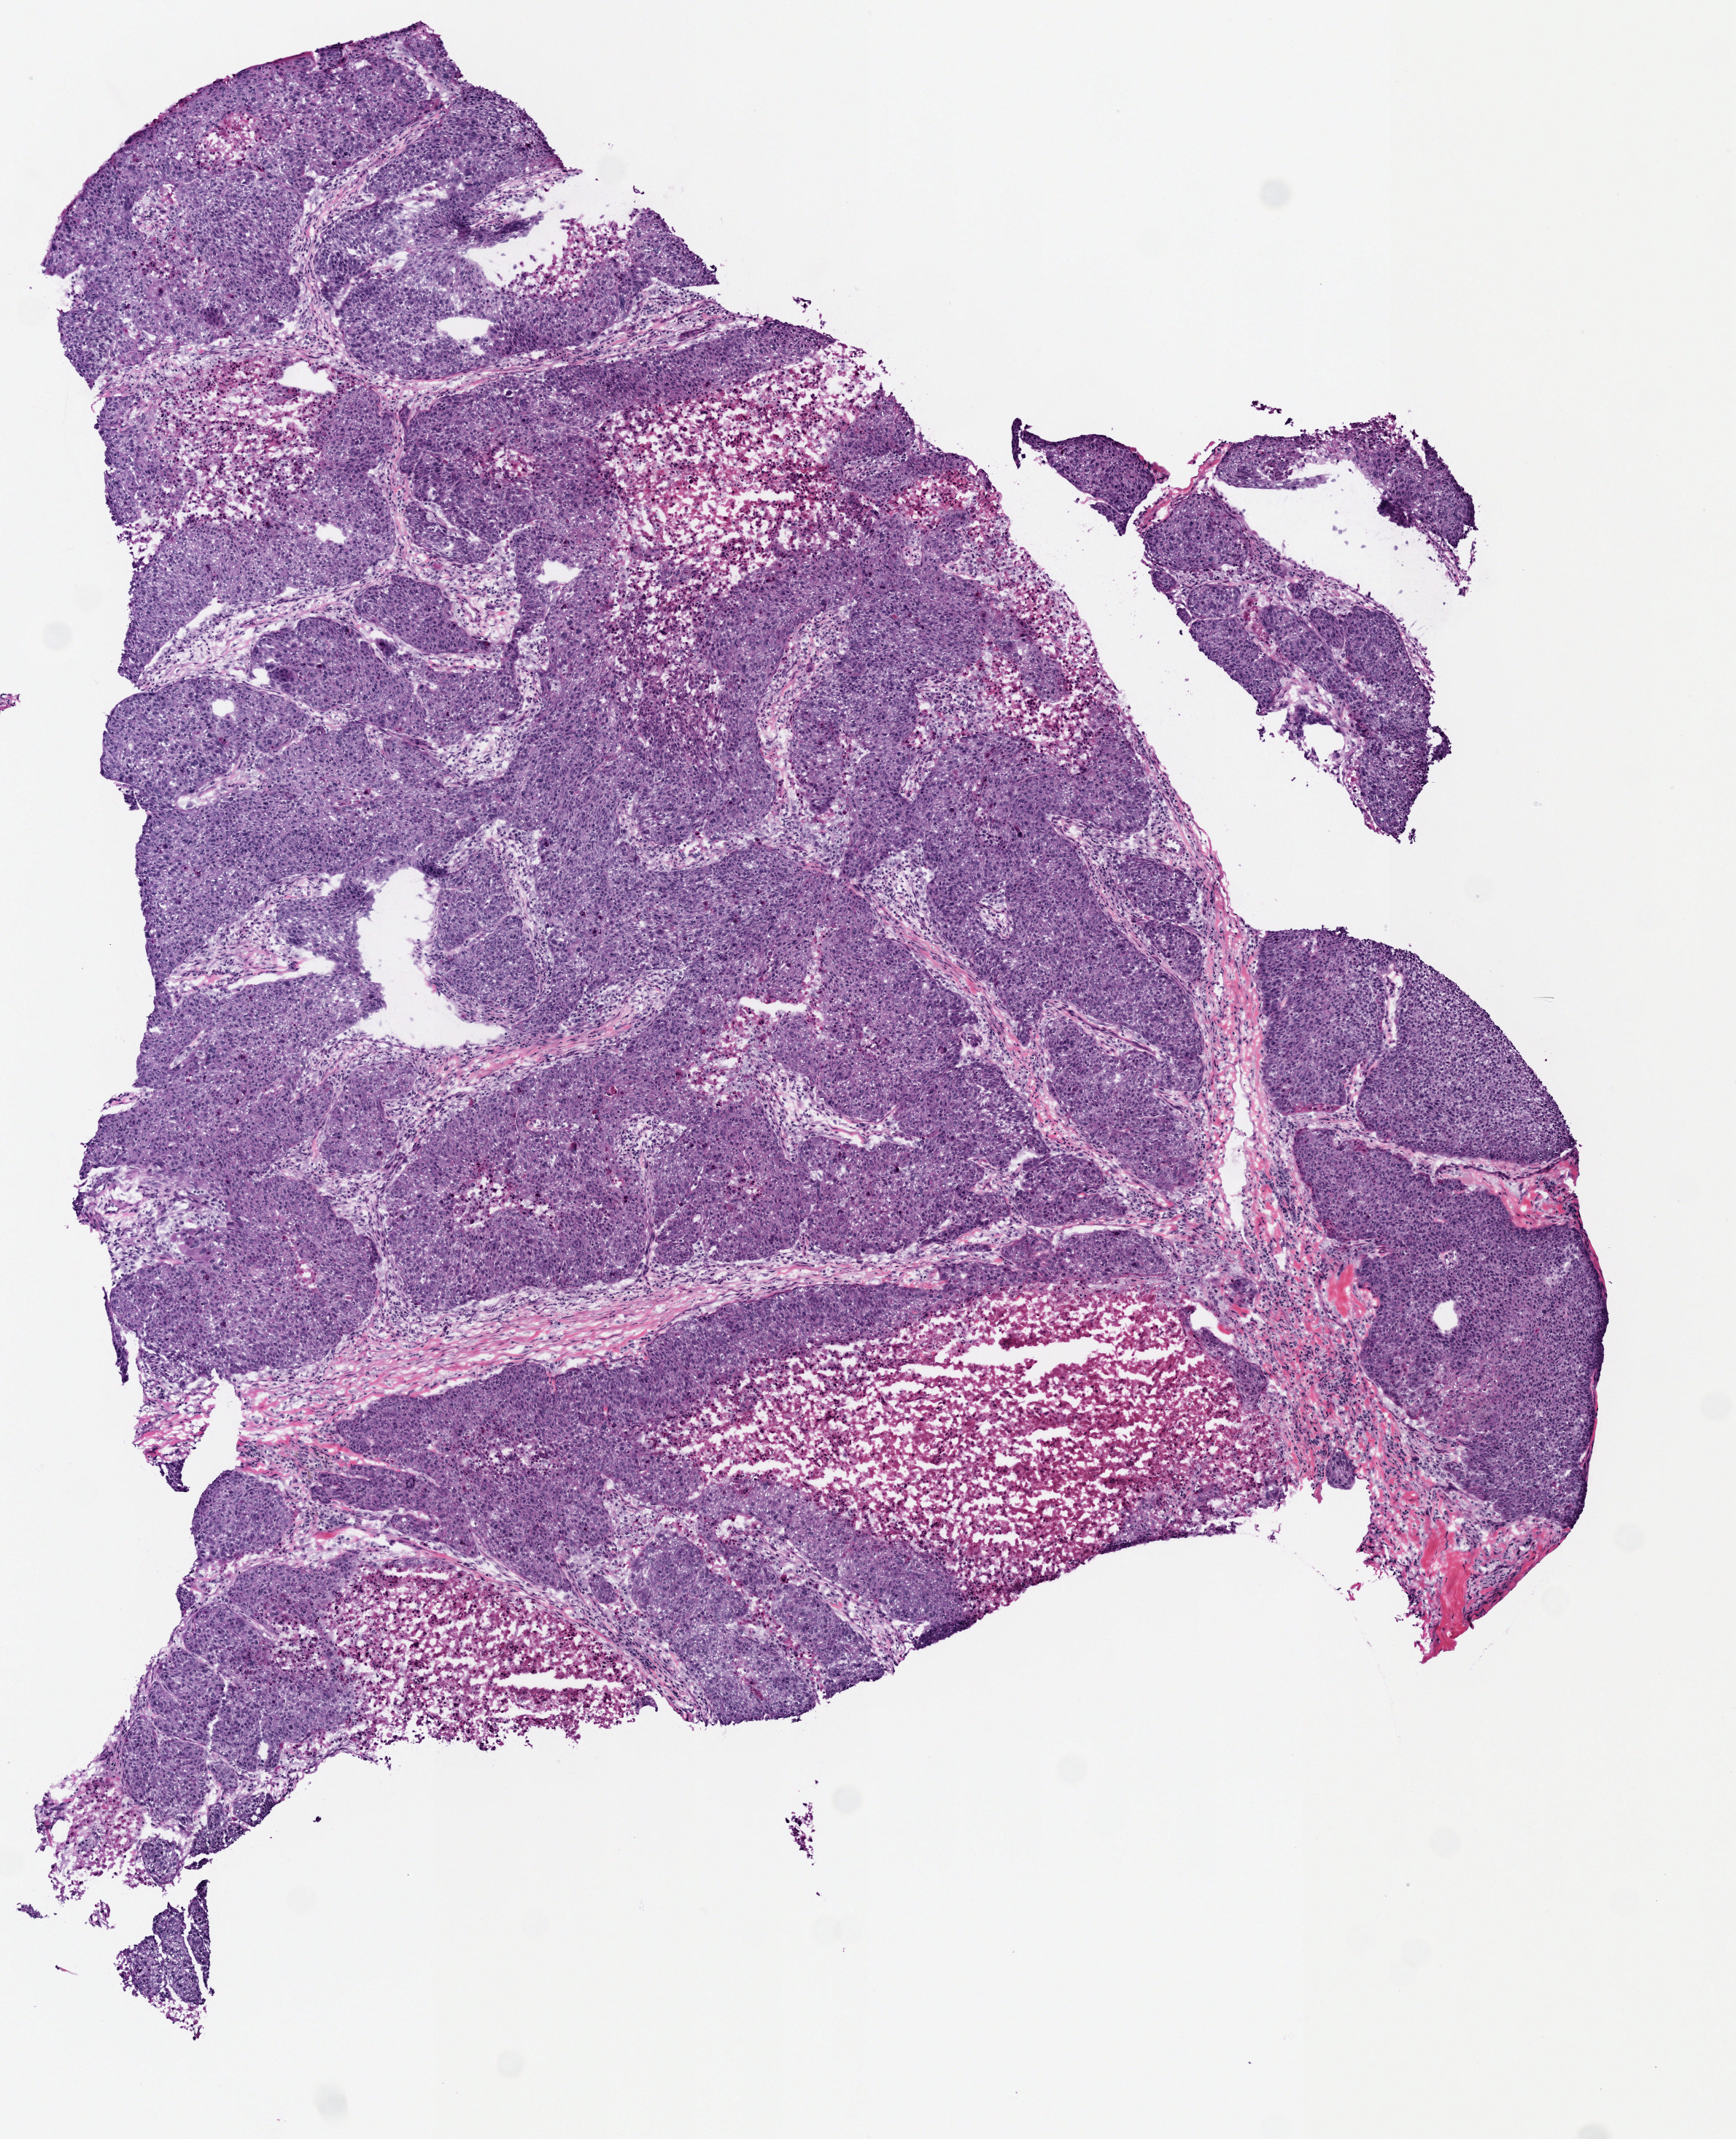
Hematoxylin and eosin (H&E) stained whole-slide image — whole scanned area (about 4.7 x 5.8 mm) shown as a low-resolution overview. Frozen section from the top of the tissue portion. Sample: primary tumour, head and neck. Male, age 49 years at initial diagnosis. Histologic grade: G2 (moderately differentiated). Composition of this section per pathologist review: tumour cells 70%, tumour nuclei 80%, normal cells 0%, stromal cells 20%, necrosis 10%. Infiltration values recorded for this section: lymphocyte infiltration 5%, monocyte infiltration 0%, neutrophil infiltration 0%.
* AJCC pathologic stage: IVA
* histologic diagnosis: Squamous cell carcinoma, NOS (upper Gum)